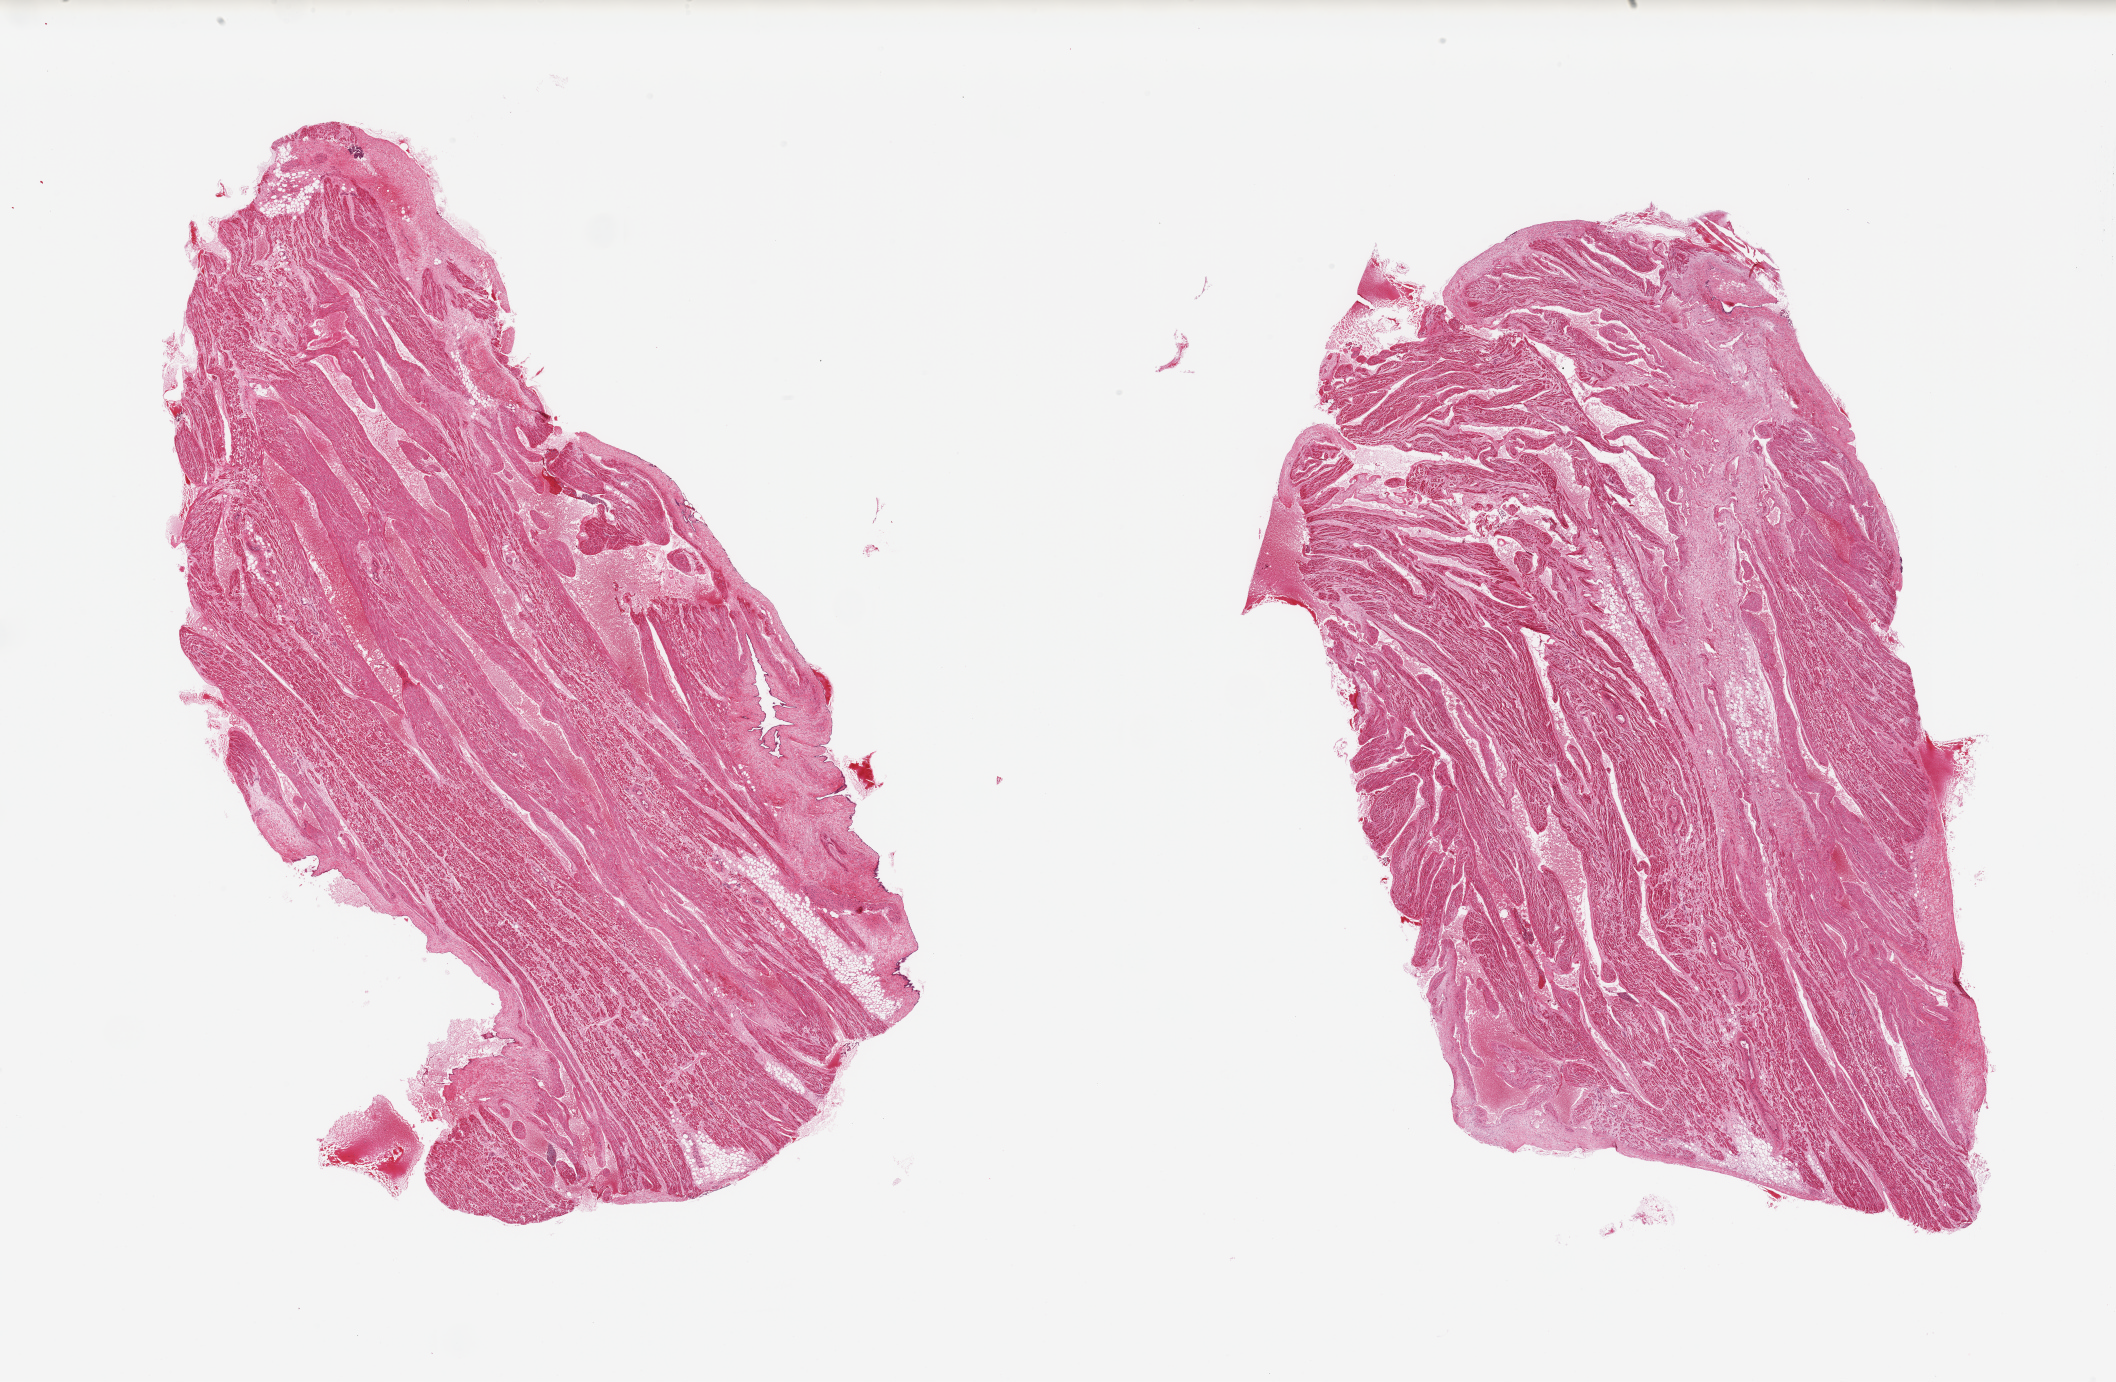
H&E whole-slide image, a low-resolution overview of the entire scanned area, about 33.5 x 21.9 mm (from a 20x scan). PAXgene-fixed, paraffin-embedded tissue. Section of auricular appendage (target tissue). Tissue donor sample. Male donor.
Pathologist's review note for this sample: 2 pieces; 10% fibrous content.